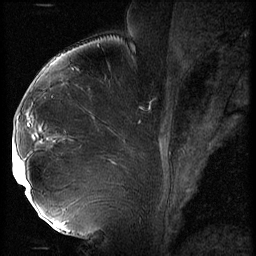
Breast MRI (dynamic contrast-enhanced), one sagittal slice. Position 34 of 56 along the scan axis. 3 images stored at this slice position (order not interpretable as contrast timing). 1.5 T. TE 4.2 ms, TR 9 ms. 2.5 mm slice thickness. 256 × 256 image matrix, field of view 180 × 180 mm. Female patient, age 43 years. From the clinical record (not read from this slice): setting: breast cancer imaged before/during neoadjuvant chemotherapy; receptor status: HER2-positive.
Outlined on this slice (semi-automatically segmented with operator editing):
- analysis volume of interest (the breast-tissue region the enhancement analysis was run in; not a lesion): bounding box [x1, y1, x2, y2] px = [13, 92, 74, 211]
- tumour enhancement mask (voxels above the 140 % enhancement threshold inside the analysis volume of interest): [13, 143, 30, 199]